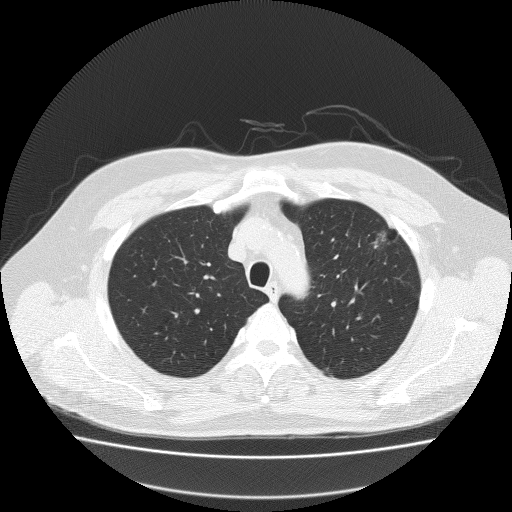
Axial slice from a low-dose chest CT screening exam; first (baseline) screen; lung window (W 1500 / L -600 HU); lung (sharp) reconstruction kernel (FC51); slice 45 of 204 in the series; 512 × 512 image matrix, field of view 410 × 410 mm. Male participant, aged 62 years at enrolment. Former smoker at enrolment.
Expert reader's lesion annotation, bounding box <347,218,414,268> (left, top, right, bottom; pixels). Reader record for this screening exam (exam-level; its link to the box is not recorded): non-calcified nodule or mass ≥4 mm, left upper lobe, 18 × 8 mm, spiculated (stellate) margins, soft tissue attenuation.